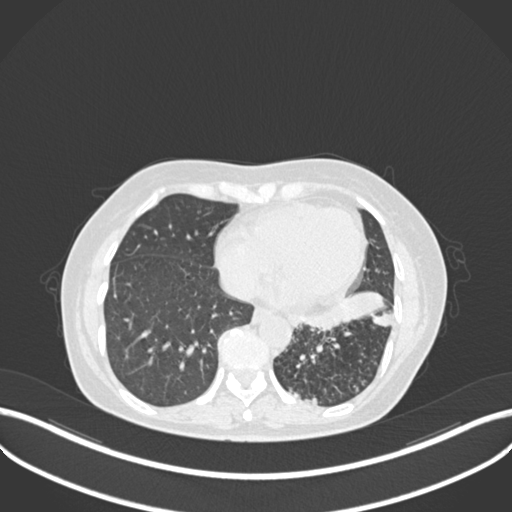
Chest CT, one axial slice; slice 90 of 270 in the series (ordered by position); reconstruction kernel B30f; lung window (W 1500 / L -600 HU); 1 mm slice thickness; 512 × 512 image matrix, field of view 400 × 400 mm. Female patient, age 63 years. Case-level facts recorded for this patient, not image findings: clinical TNM (as recorded): T1b N0 M0.
Structures marked on this image (bounding box drawn by a radiologist):
- lung tumour (recorded histology: adenocarcinoma): bounding box <299,291,393,335> (left, top, right, bottom; pixels)